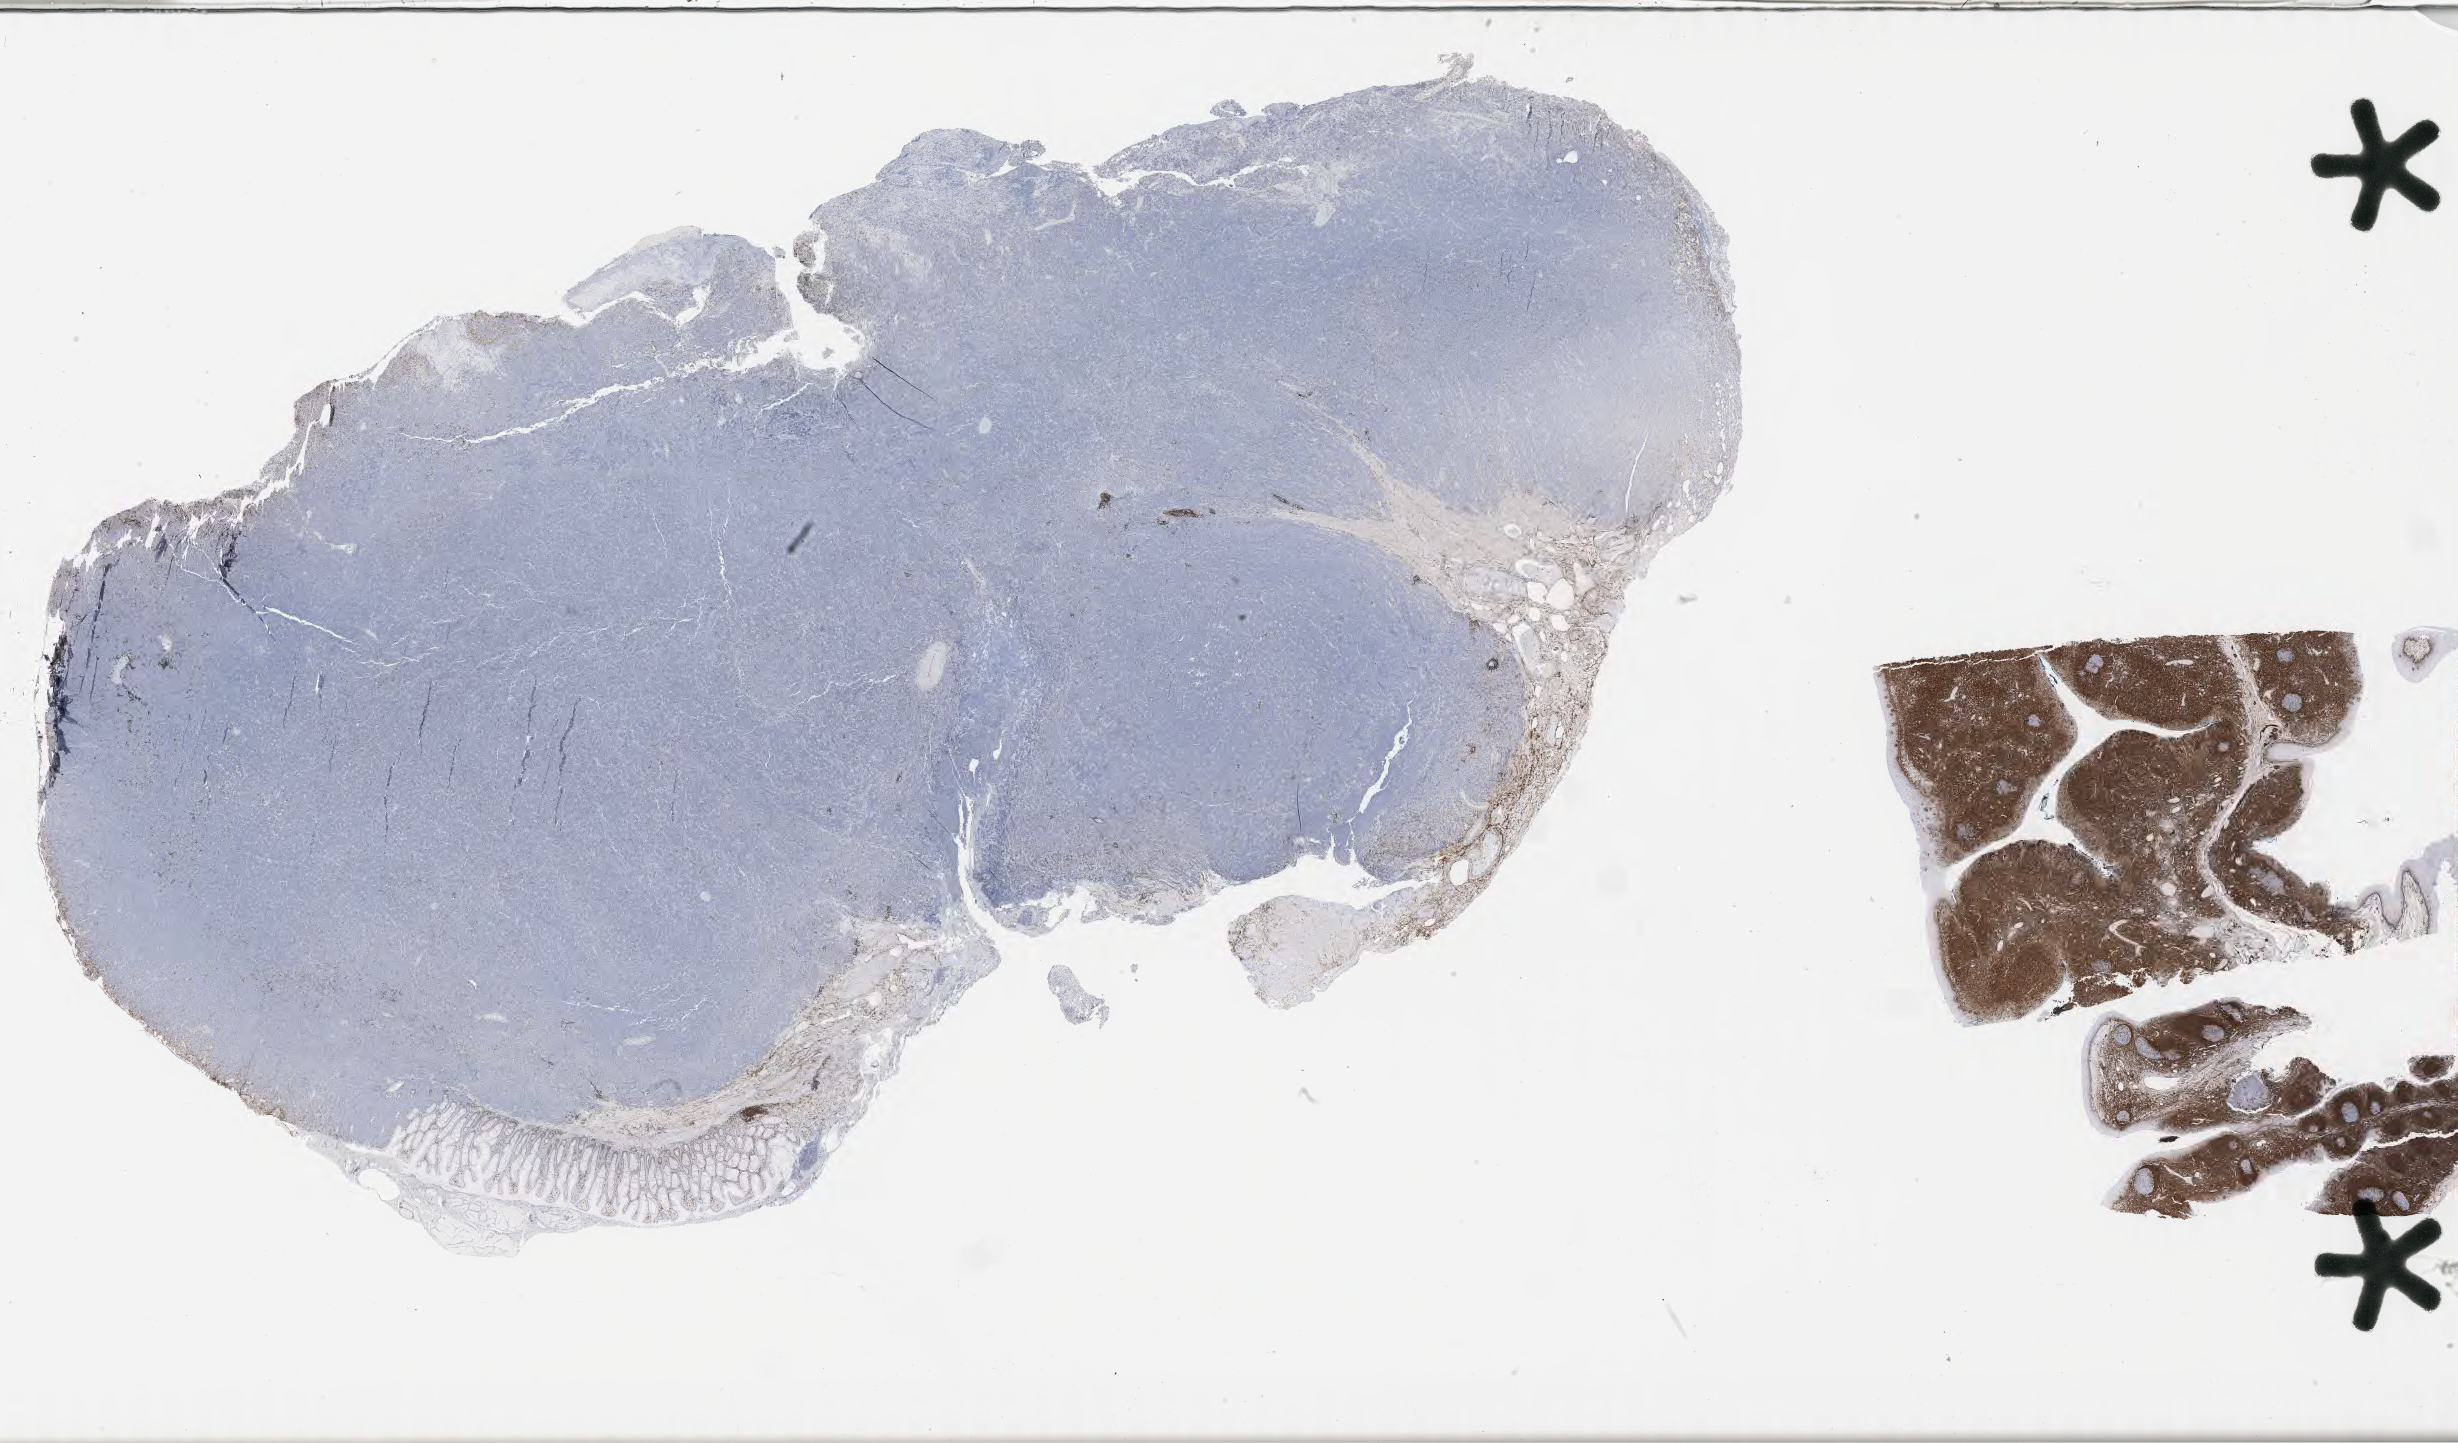
IHC for BCL2, whole-slide image, low-resolution overview of the scanned area, about 39.7 x 23.3 mm; specimen: tumor tissue. Patient female; aged 29.
Histologic diagnosis: Burkitt lymphoma, NOS.